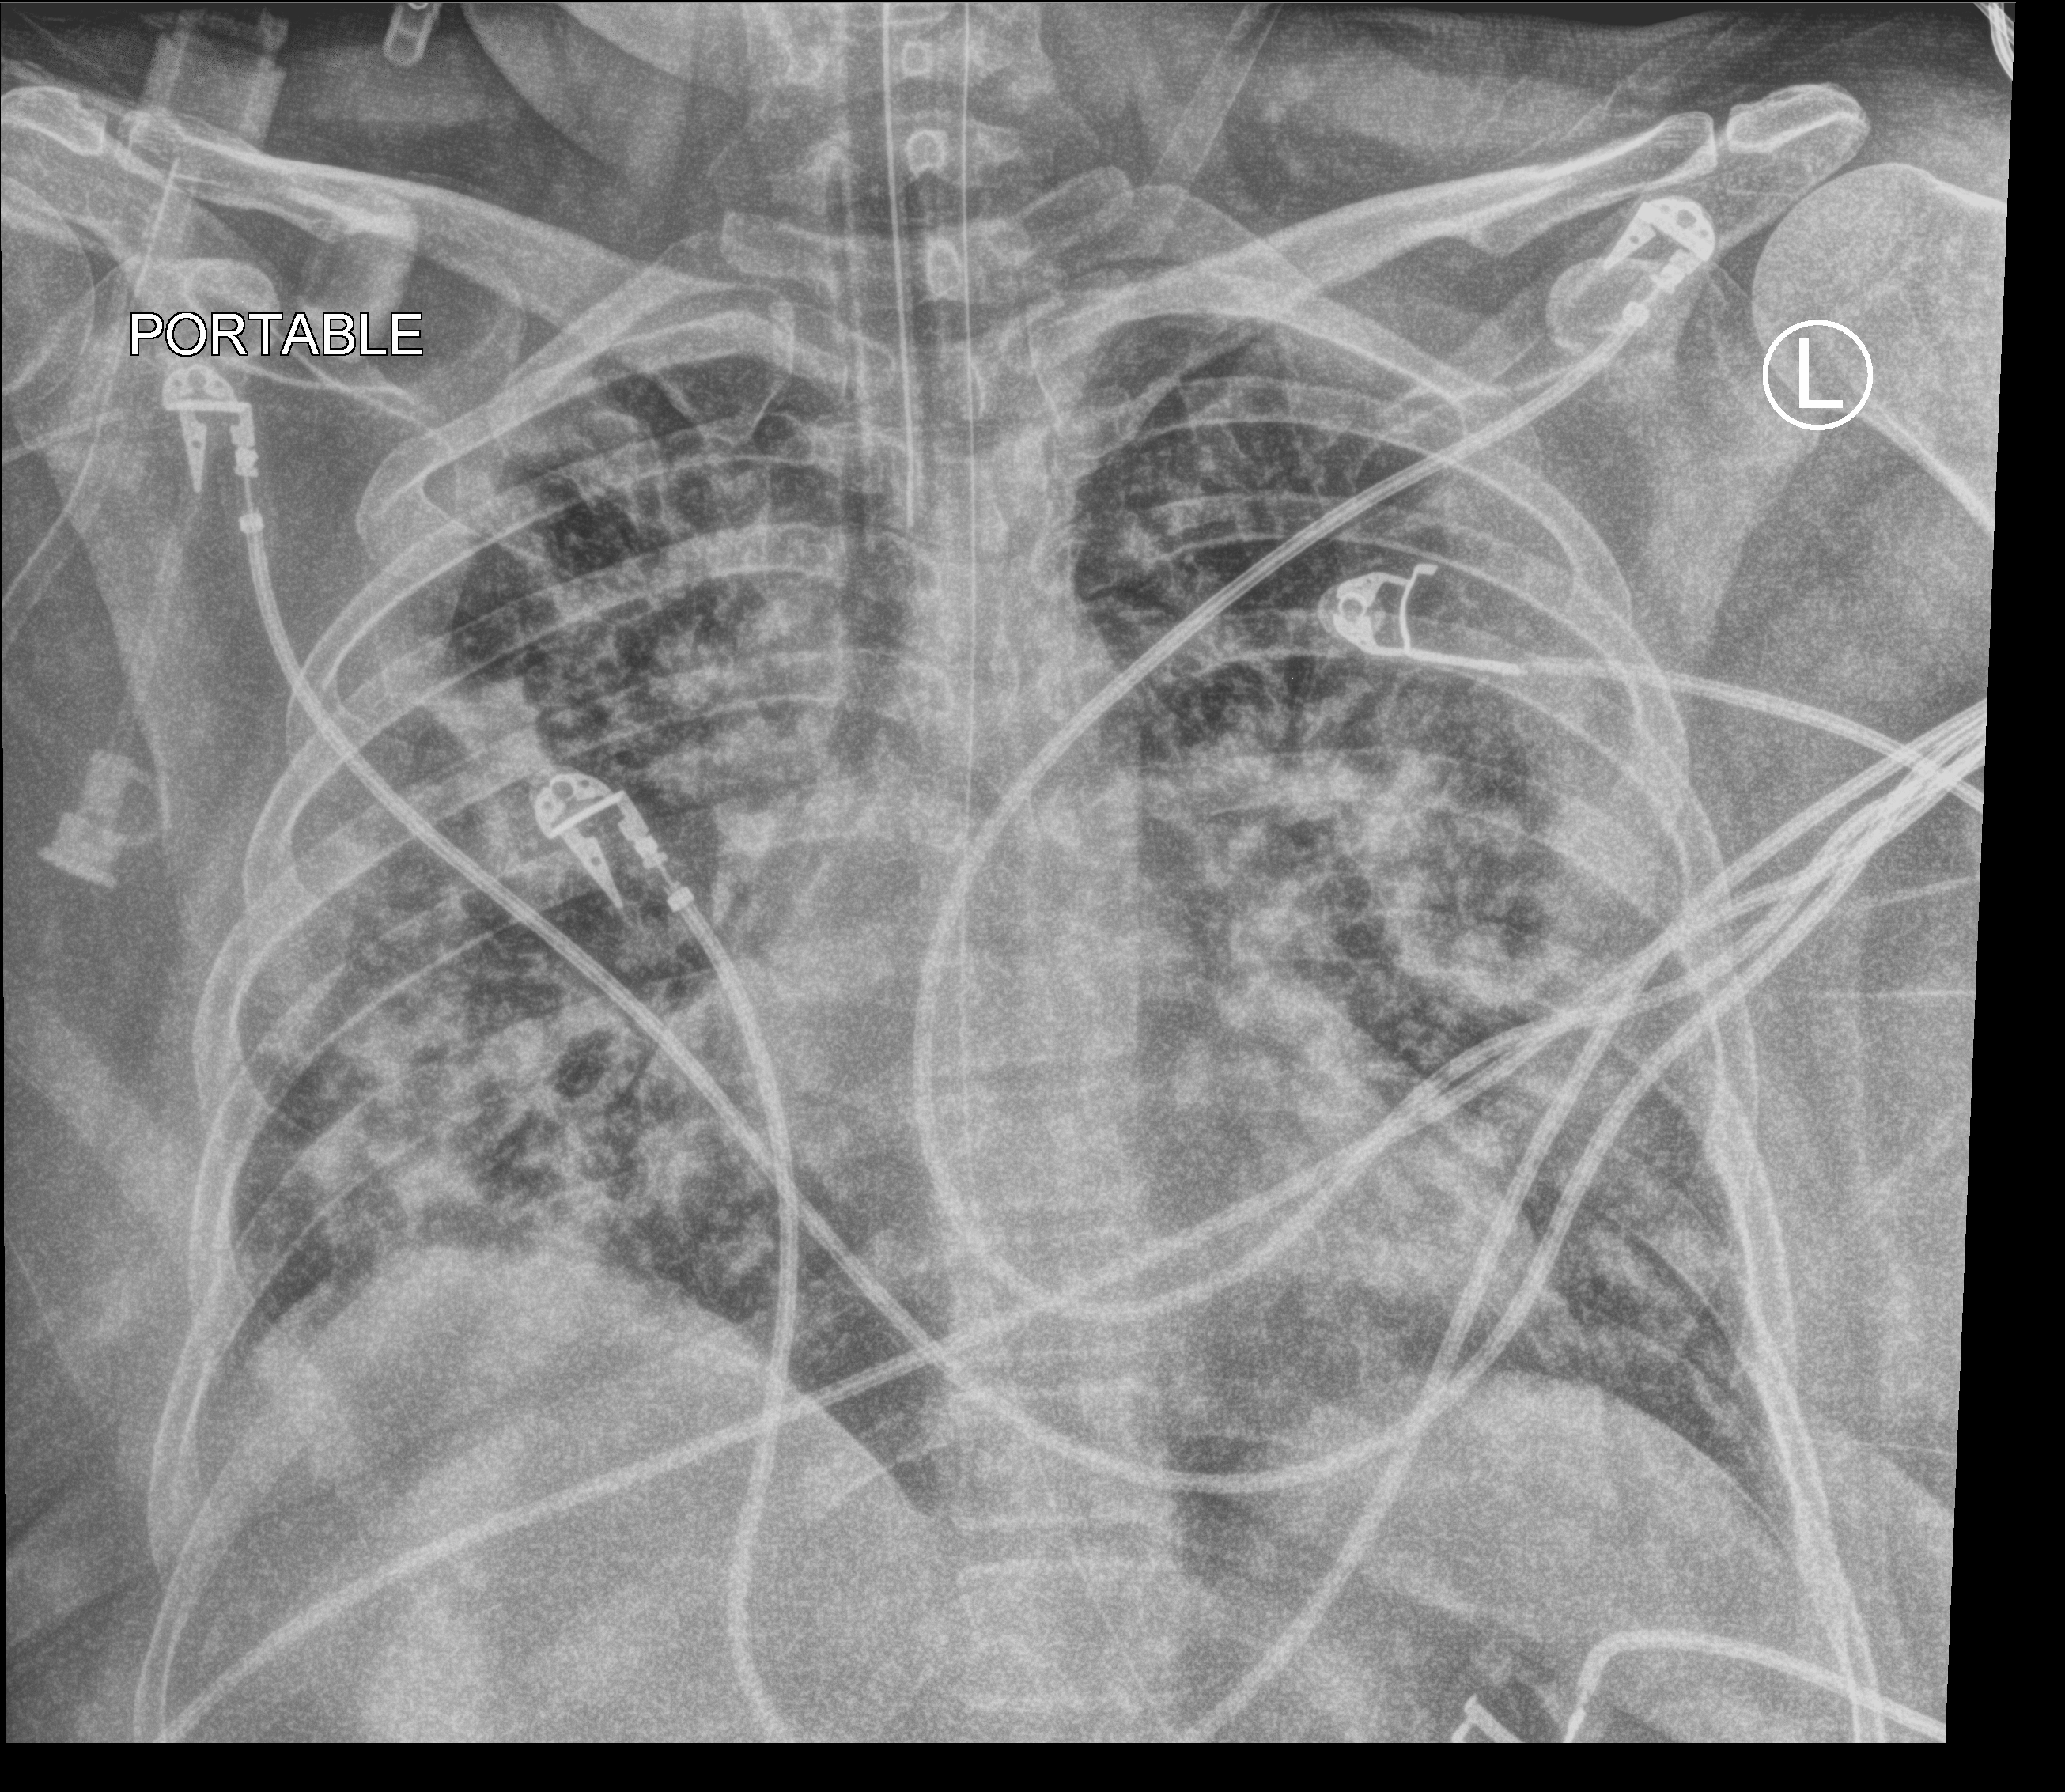
Chest X-ray (portable); anteroposterior (AP) projection. Patient hospitalised with COVID-19; female, aged 18–59 years.
From the hospital-stay record, not from the radiograph (when in the stay this image was taken is not recorded): admitted to intensive care during this hospital stay: yes.